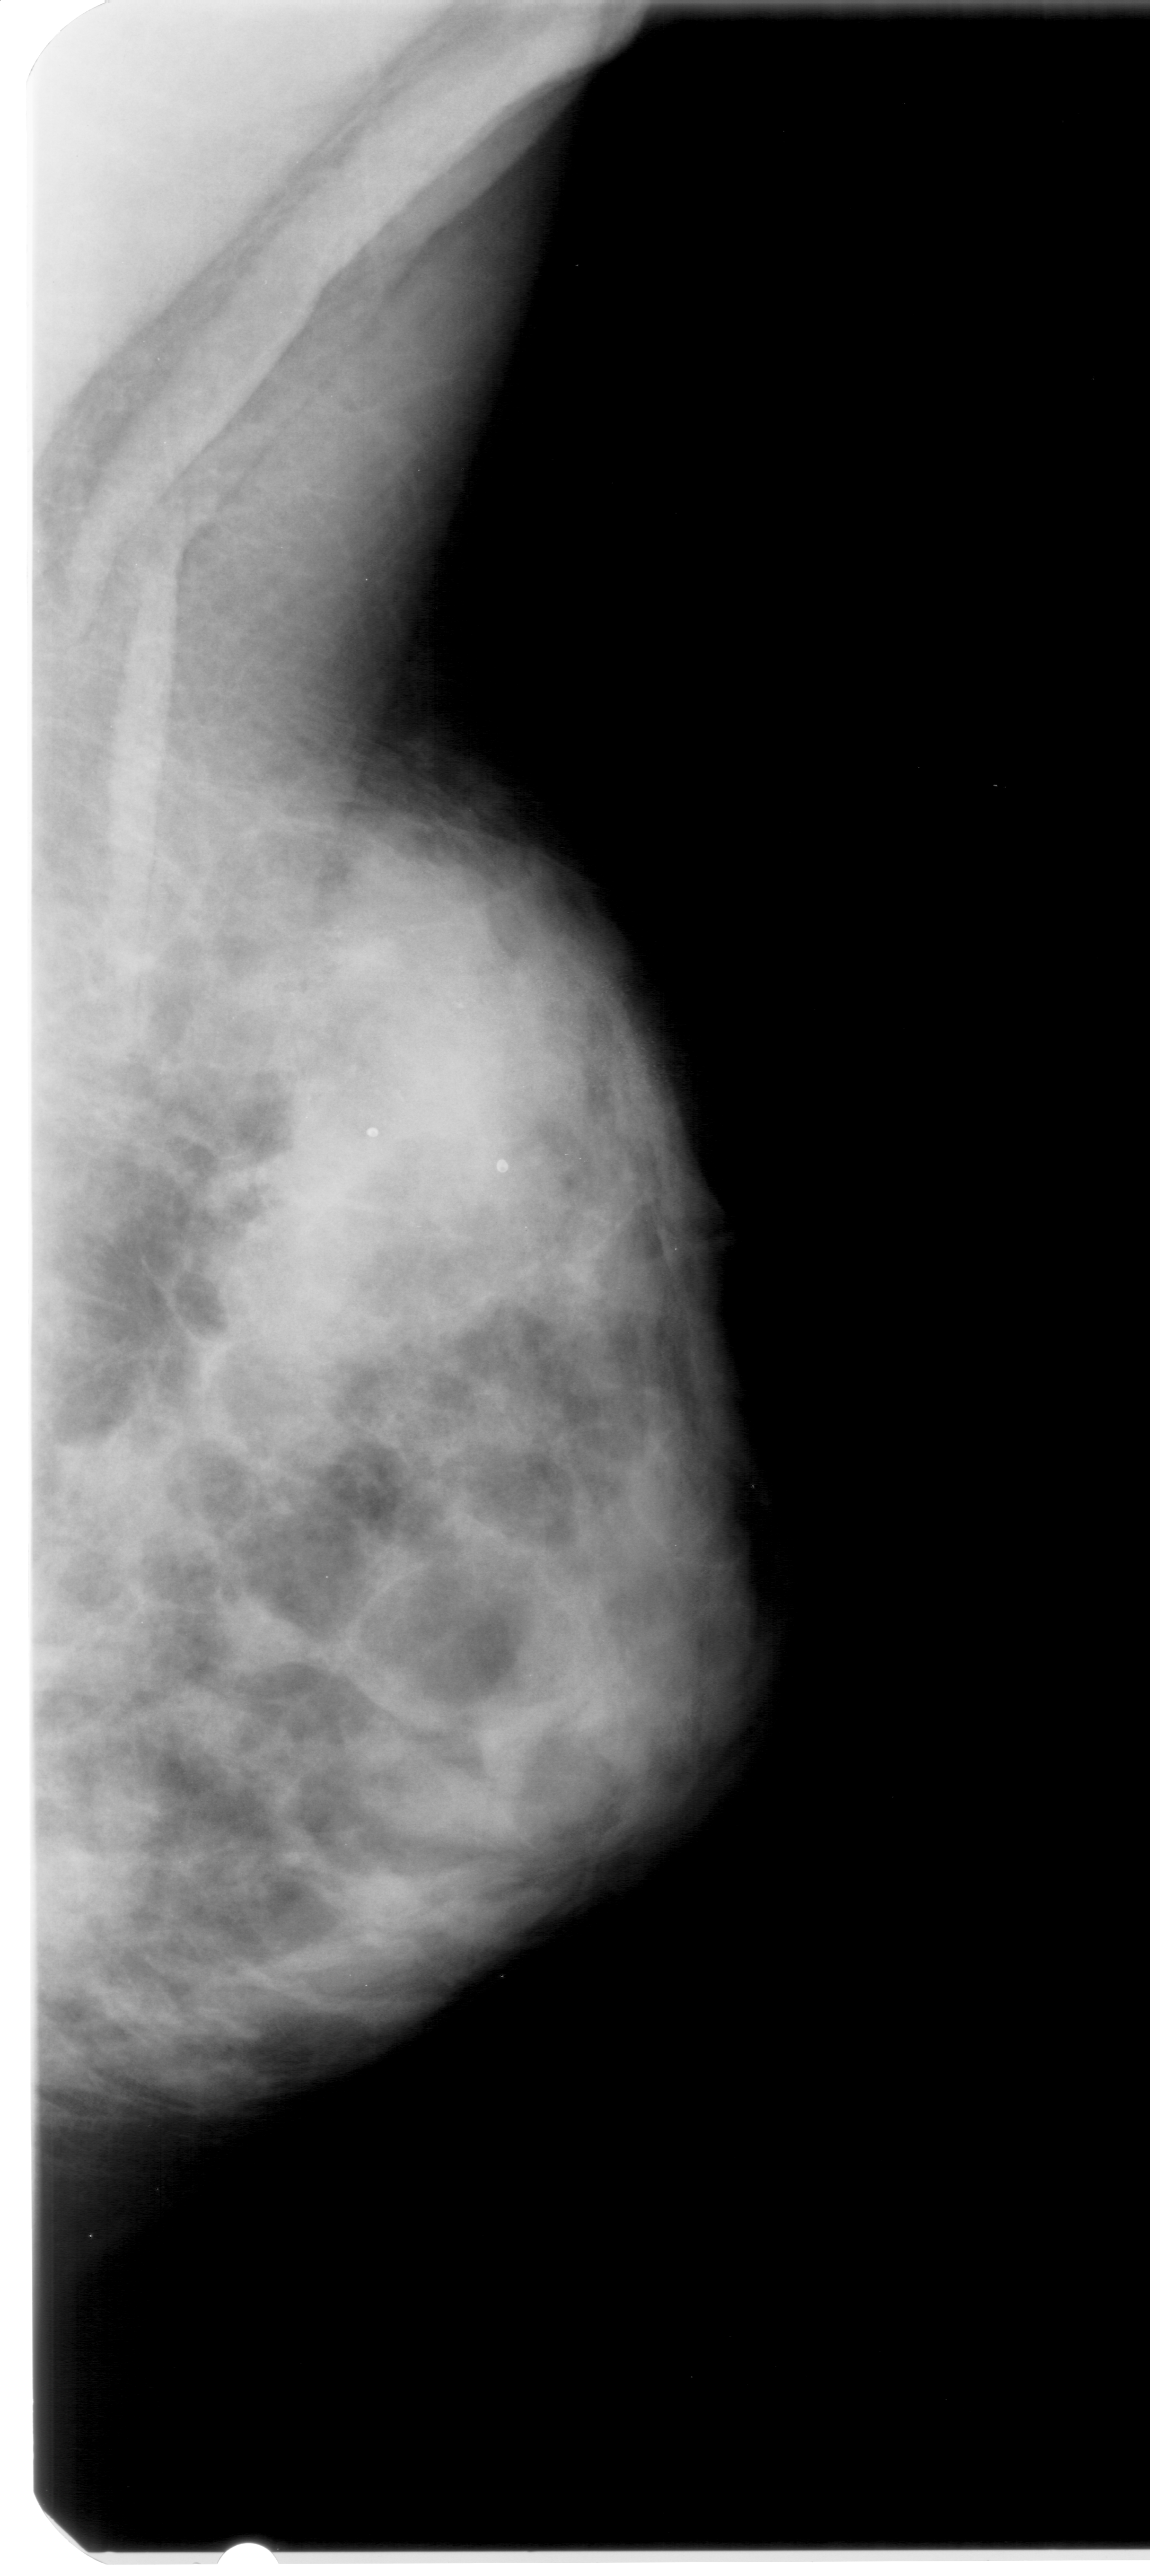
Digitized screen-film mammogram, right breast, MLO view, BI-RADS breast density category 4 (scale 1–4).
- Marked abnormality: calcifications, morphology punctate, distribution segmental; BI-RADS assessment category 4; pathology (as recorded): benign.